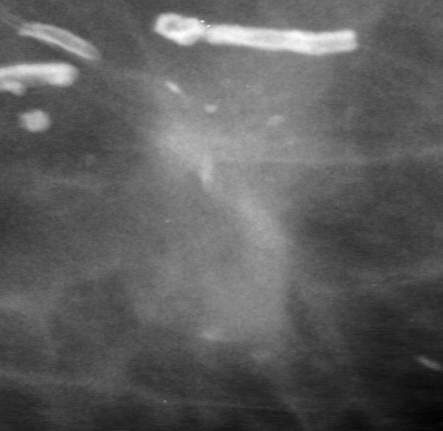
Crop from a digitized film mammogram around one marked abnormality; left breast; MLO view.
Marked abnormality: mass, shape irregular, margins ill defined; BI-RADS assessment category 3; subtlety rating 3 on a 1 (subtle) to 5 (obvious) scale; pathology result (as recorded, not read from the image): malignant.